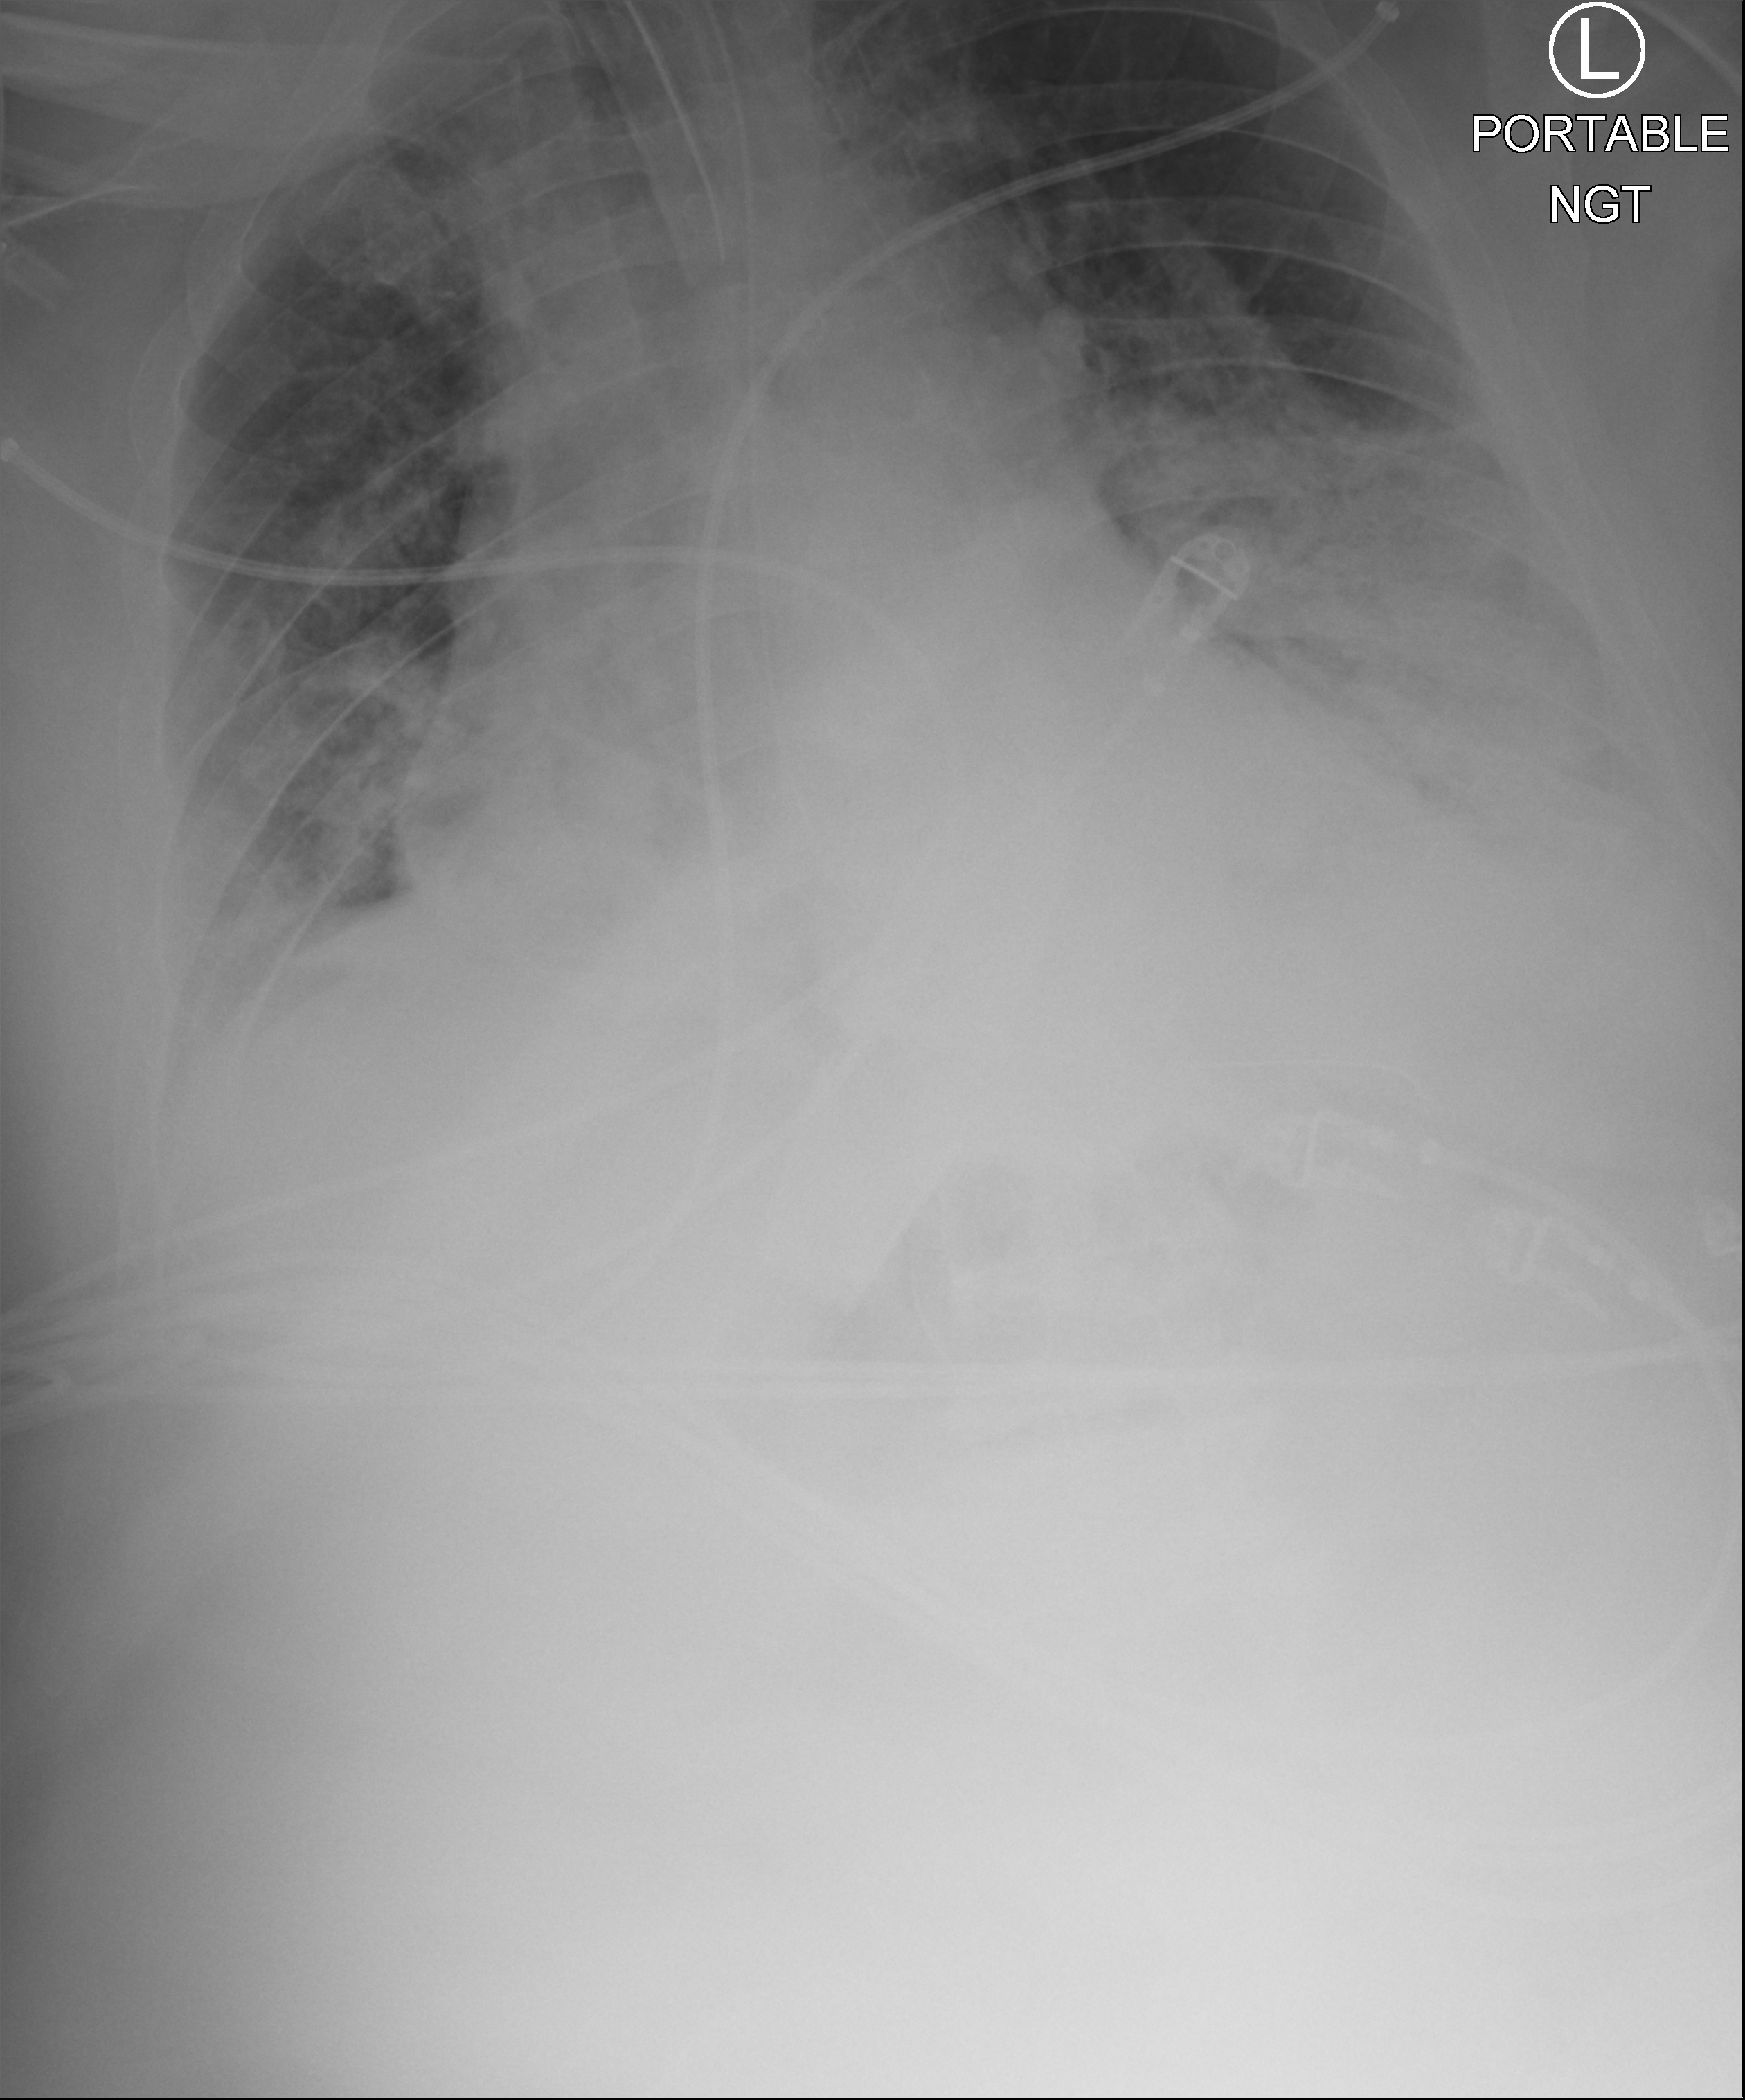
Portable chest radiograph; anteroposterior (AP) projection. Patient hospitalised with COVID-19; male, aged 60–74 years.
Admission-level facts for this patient (not findings on this image; timing relative to this image not recorded):
- admitted to intensive care during this hospital stay: yes